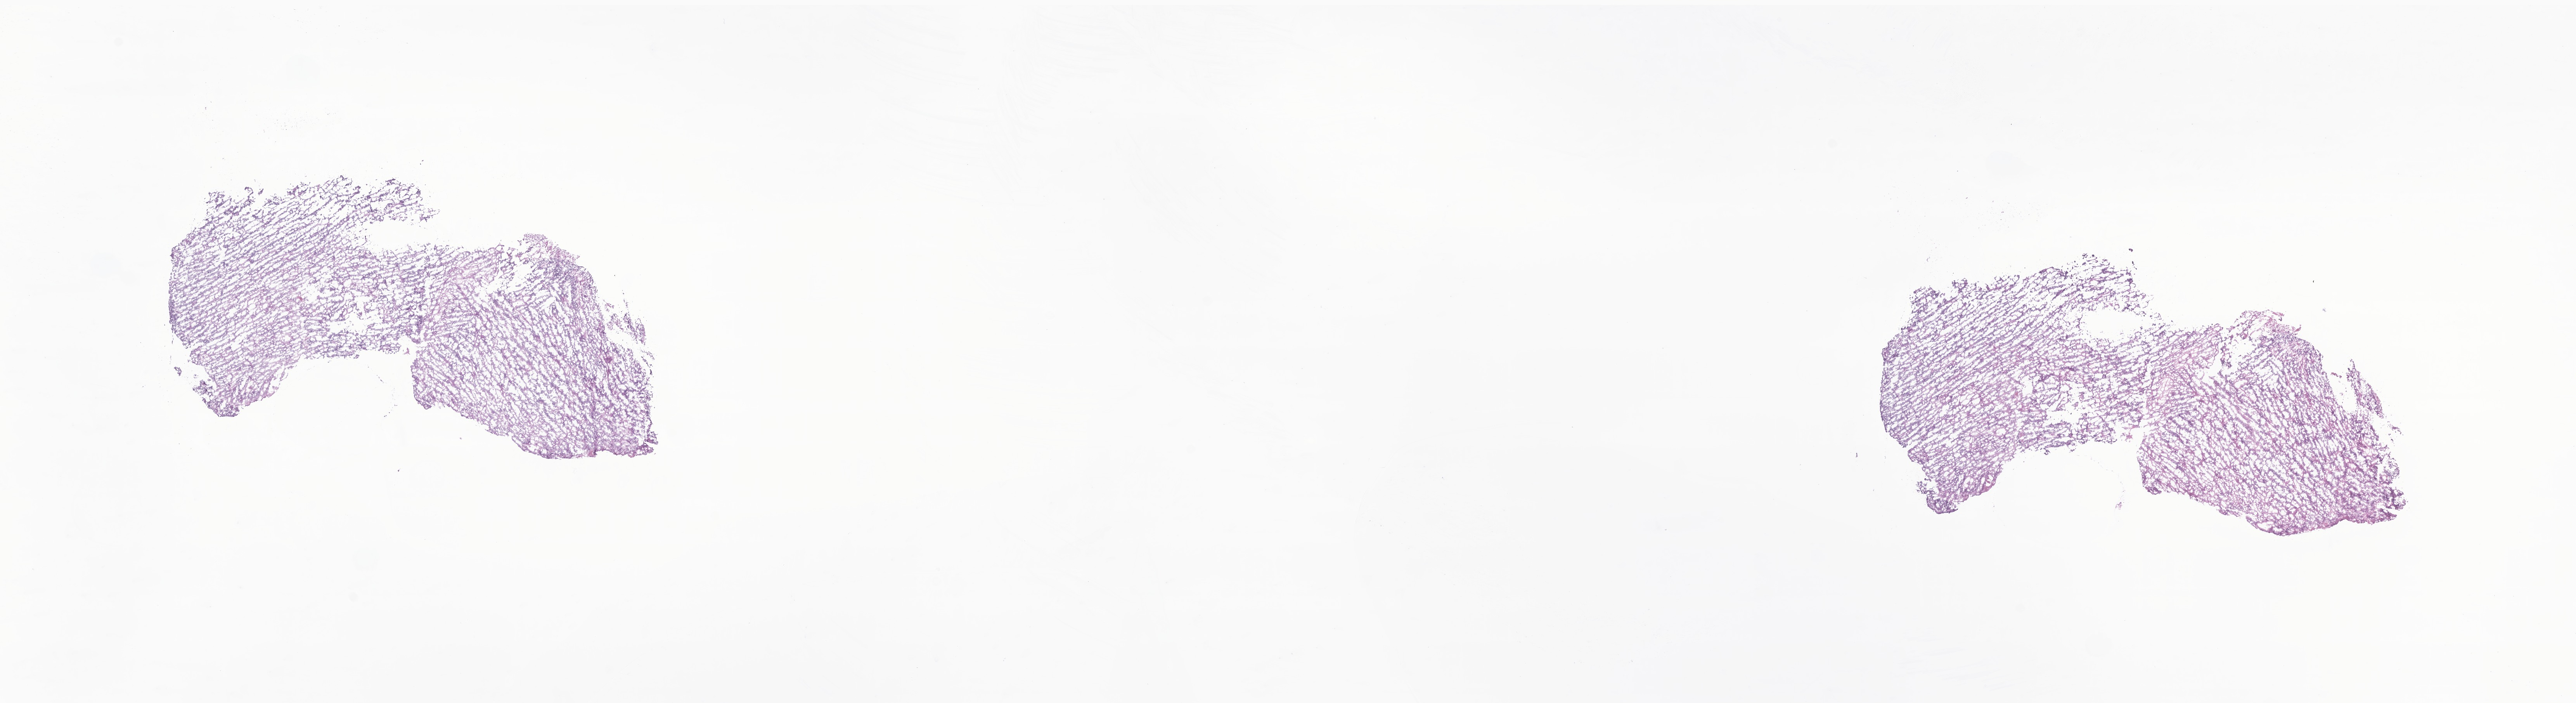
Hematoxylin and eosin (H&E) whole-slide image of tumor tissue from the brain, whole scanned area (about 28.0 x 7.6 mm) shown as a low-resolution overview. Frozen section. Patient male; age 198 days.
- recorded diagnosis: Ependymoma, NOS